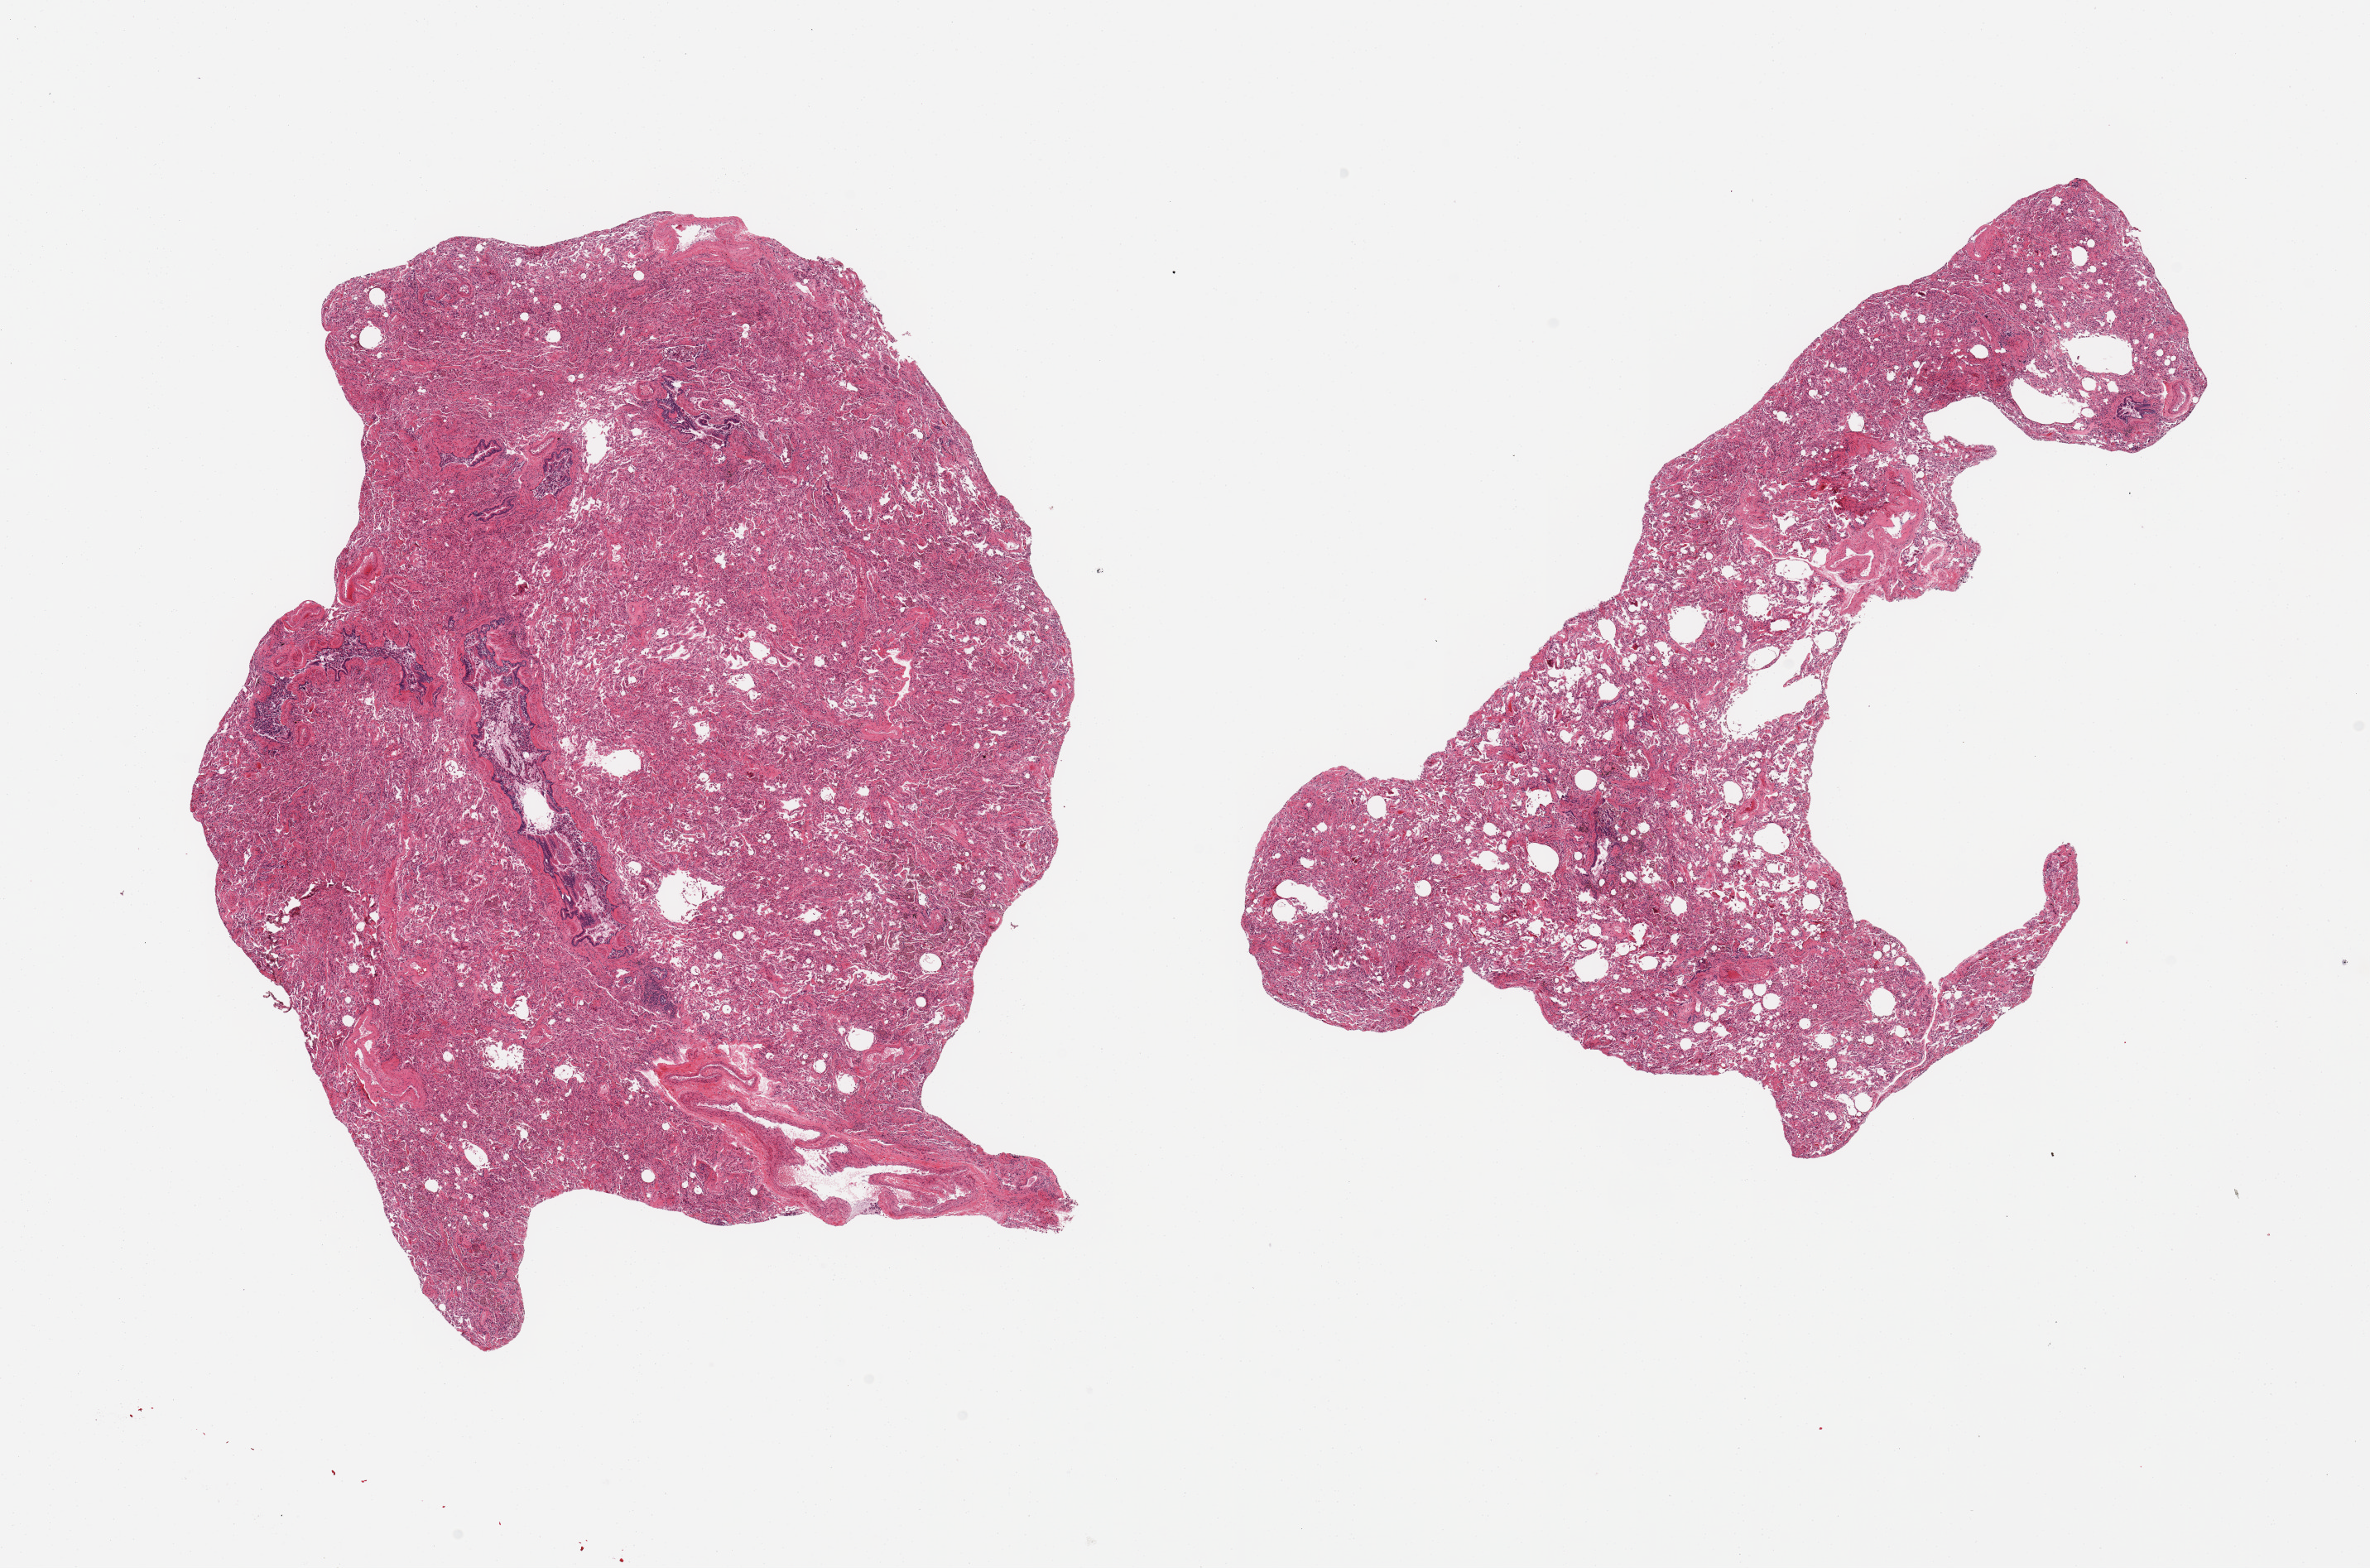
Hematoxylin and eosin (H&E) whole-slide image — shown as a low-resolution overview of the whole scanned area (about 22.6 x 15.0 mm); PAXgene-fixed, paraffin-embedded tissue; target tissue: lung; tissue donor sample. Donor sex: female.
Review note (as recorded): 2 pieces, moderate congestion, abundant hemosiderin laden macrophages.